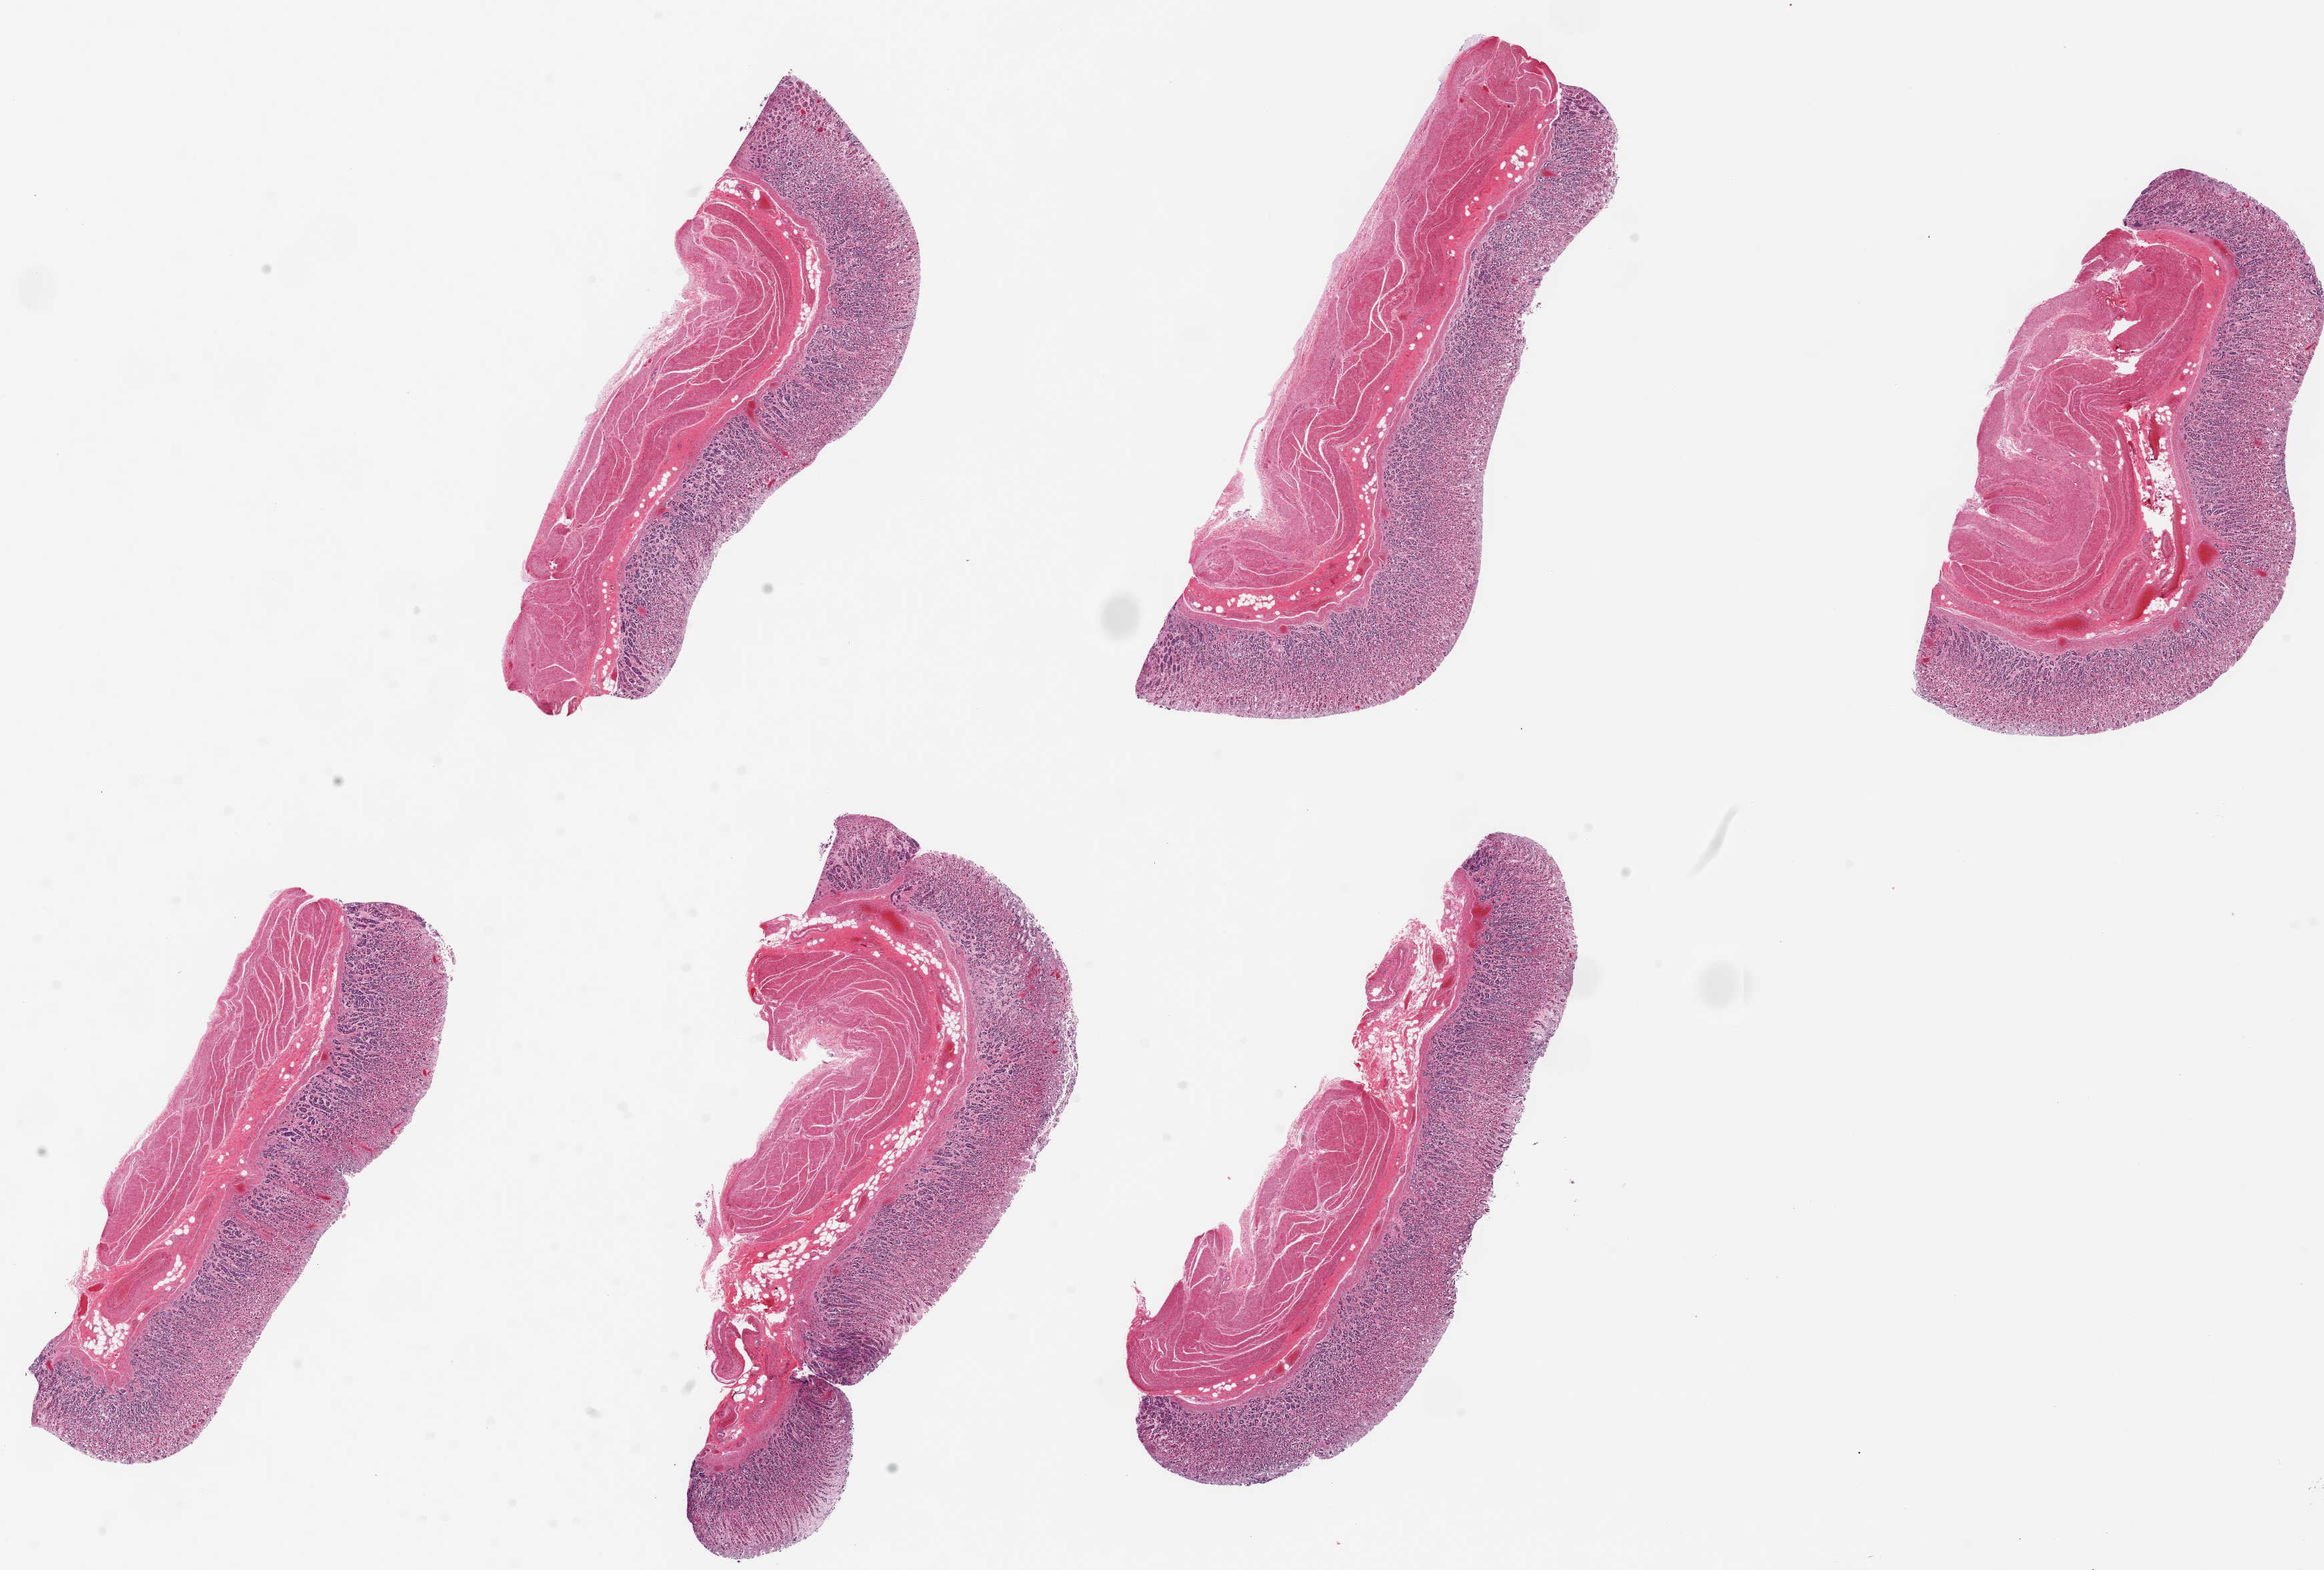
Whole-slide image, H&E stain, whole scanned area (about 27.6 x 18.6 mm, slide scanned at 20x) shown as a low-resolution overview; PAXgene-fixed, paraffin-embedded tissue; sampled site (target tissue): stomach; donor tissue sample. Donor sex: male.
Review note (as recorded): 6 pieces, up to 9x4mm; mucosa ~40% thickness, moderately autolyzed.